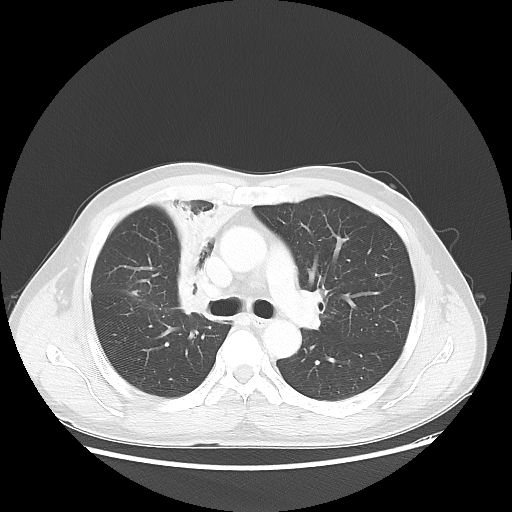
Chest CT, one axial slice. Slice 34 of 56 in the series (ordered by position). Reconstruction kernel LUNG. Lung window (W 1500 / L -600 HU). 512 × 512 image matrix. Patient: male, 60 years. From the clinical record (not read from this slice): clinical TNM (as recorded): T2a N1 M0.
Outlined on this slice (rectangle marked by the reading radiologist):
- lung tumour (recorded histology: squamous cell carcinoma): bounding box (x1, y1, x2, y2) in pixels: (164, 200, 232, 318)